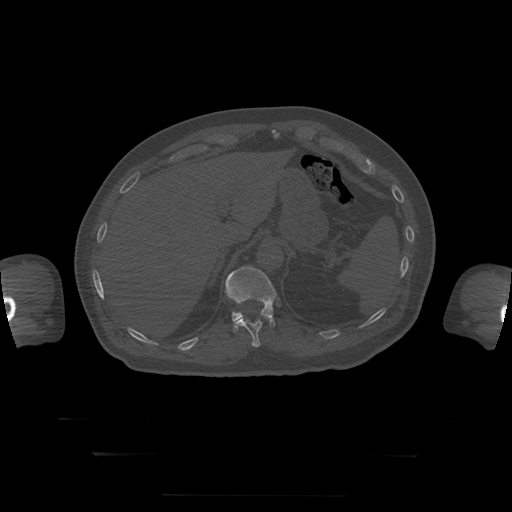
CT including the spine, one axial slice. Position 87 of 397 along the scan axis. Reconstruction kernel STANDARD. 120 kVp. Bone window (W 1800 / L 400 HU). 1.25 mm slice thickness. 512 × 512 image matrix, field of view 510 × 510 mm. Patient age 73 years. From the clinical record (not read from this slice): primary cancer: prostate.
Structures marked on this image (semi-automatically segmented with operator editing):
- T11 vertebra: bounding box [x1, y1, x2, y2] px = [235, 314, 276, 347]
- T12 vertebra: [226, 267, 277, 333]